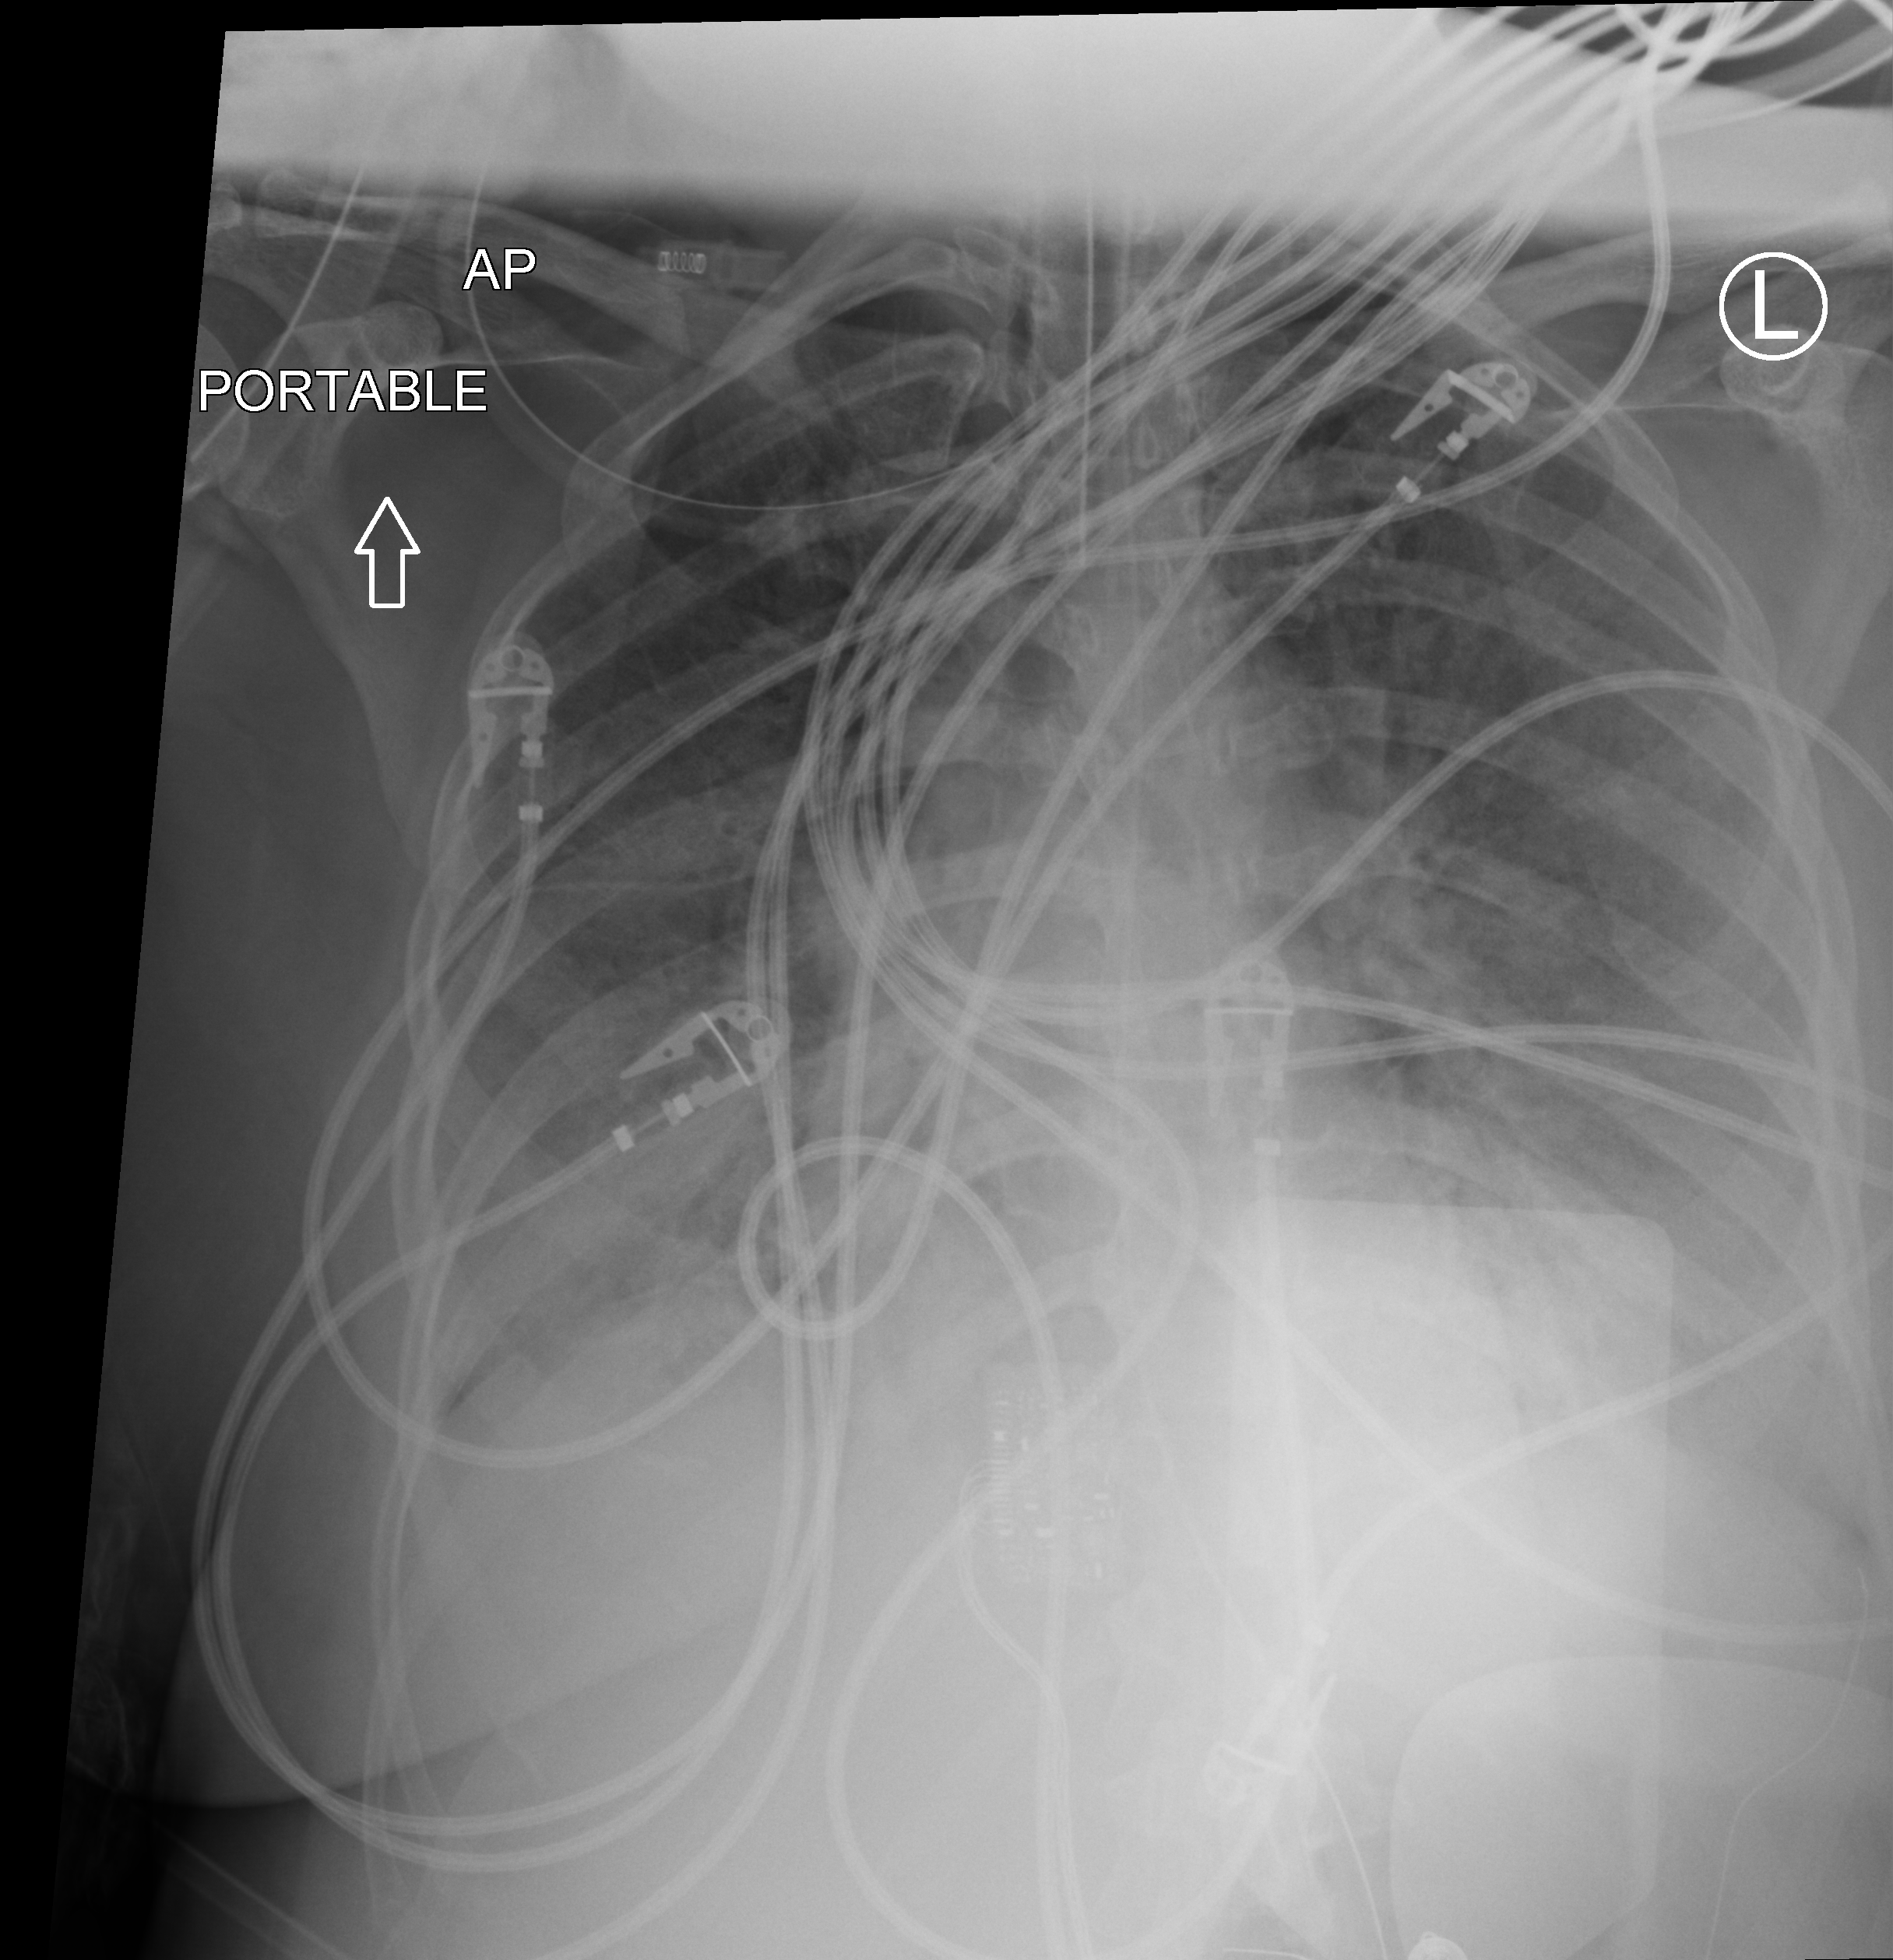
Bedside chest radiograph (computed radiography); anteroposterior (AP) projection. Patient hospitalised with COVID-19; male, aged 18–59 years.
Admission-level facts for this patient (not findings on this image; timing relative to this image not recorded):
- length of hospital stay: 38 days
- COPD (admission record): no
- mechanically ventilated during this hospital stay: yes